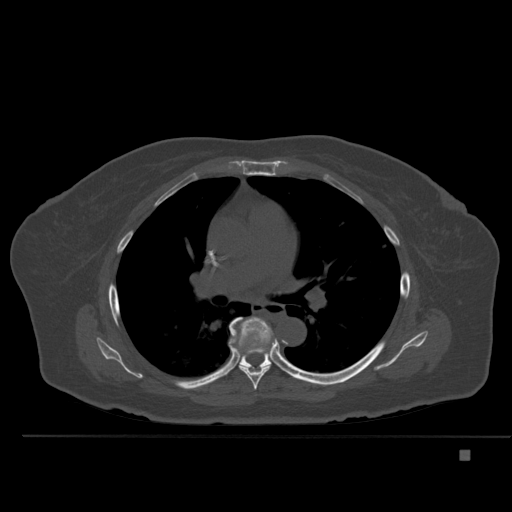
CT including the spine, one axial slice; position 334 of 477 along the scan axis; bone window (W 1800 / L 400 HU); 1.5 mm slice thickness; 512 × 512 image matrix, field of view 422 × 422 mm. Female patient, age 74 years. From the clinical record (not read from this slice): primary cancer: colon.
Annotated regions visible in this slice (semi-automatically segmented with operator editing):
- T6 vertebra: bounding box [x1, y1, x2, y2] px = [239, 350, 271, 390]
- T7 vertebra: [229, 316, 274, 369]